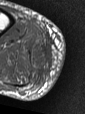
MRI of an extremity soft-tissue mass, one axial slice. Slice 10 of 47 in the series (ordered by position). MR volume resampled by the dataset authors to the PET/CT grid (not the native acquisition matrix). 3.27 mm slice thickness. 85 × 114 image matrix, field of view 83 × 111 mm. Male patient. From the clinical record (not read from this slice): histological type: pleiomorphic liposarcoma; grade: high; site of the primary tumour: right calf.
Outlined on this slice (expert contour drawn on MRI and transferred to this co-registered scan by the dataset authors):
- gross tumour volume including surrounding oedema: box from (x=31, y=46) to (x=46, y=67) px